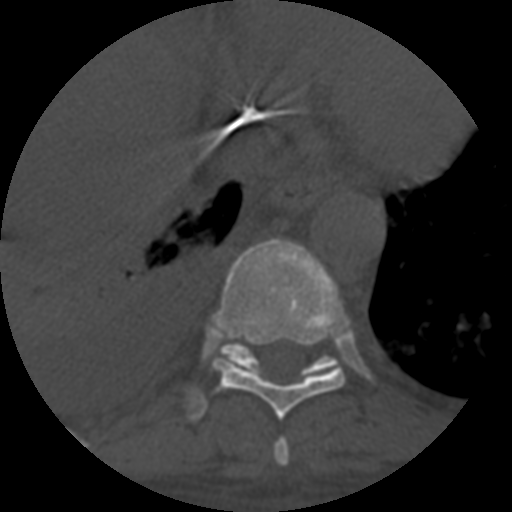
CT including the spine, one axial slice; slice 373 of 708 in the series (ordered by position); reconstruction kernel STANDARD; 120 kVp; one of 3 acquisitions stored at this slice position; bone window (W 1800 / L 400 HU); 1.25 mm slice thickness; 512 × 512 image matrix. Patient age 55 years. Case-level facts recorded for this patient, not image findings: primary cancer: colon; vertebrae with lytic lesions (as recorded): T12, L1, L5.
Outlined on this slice (semi-automatically segmented with operator editing):
- T10 vertebra: box from (x=221, y=344) to (x=337, y=379) px
- T8 vertebra: (x=274, y=438)–(x=289, y=466)
- T9 vertebra: (x=188, y=239)–(x=348, y=420)